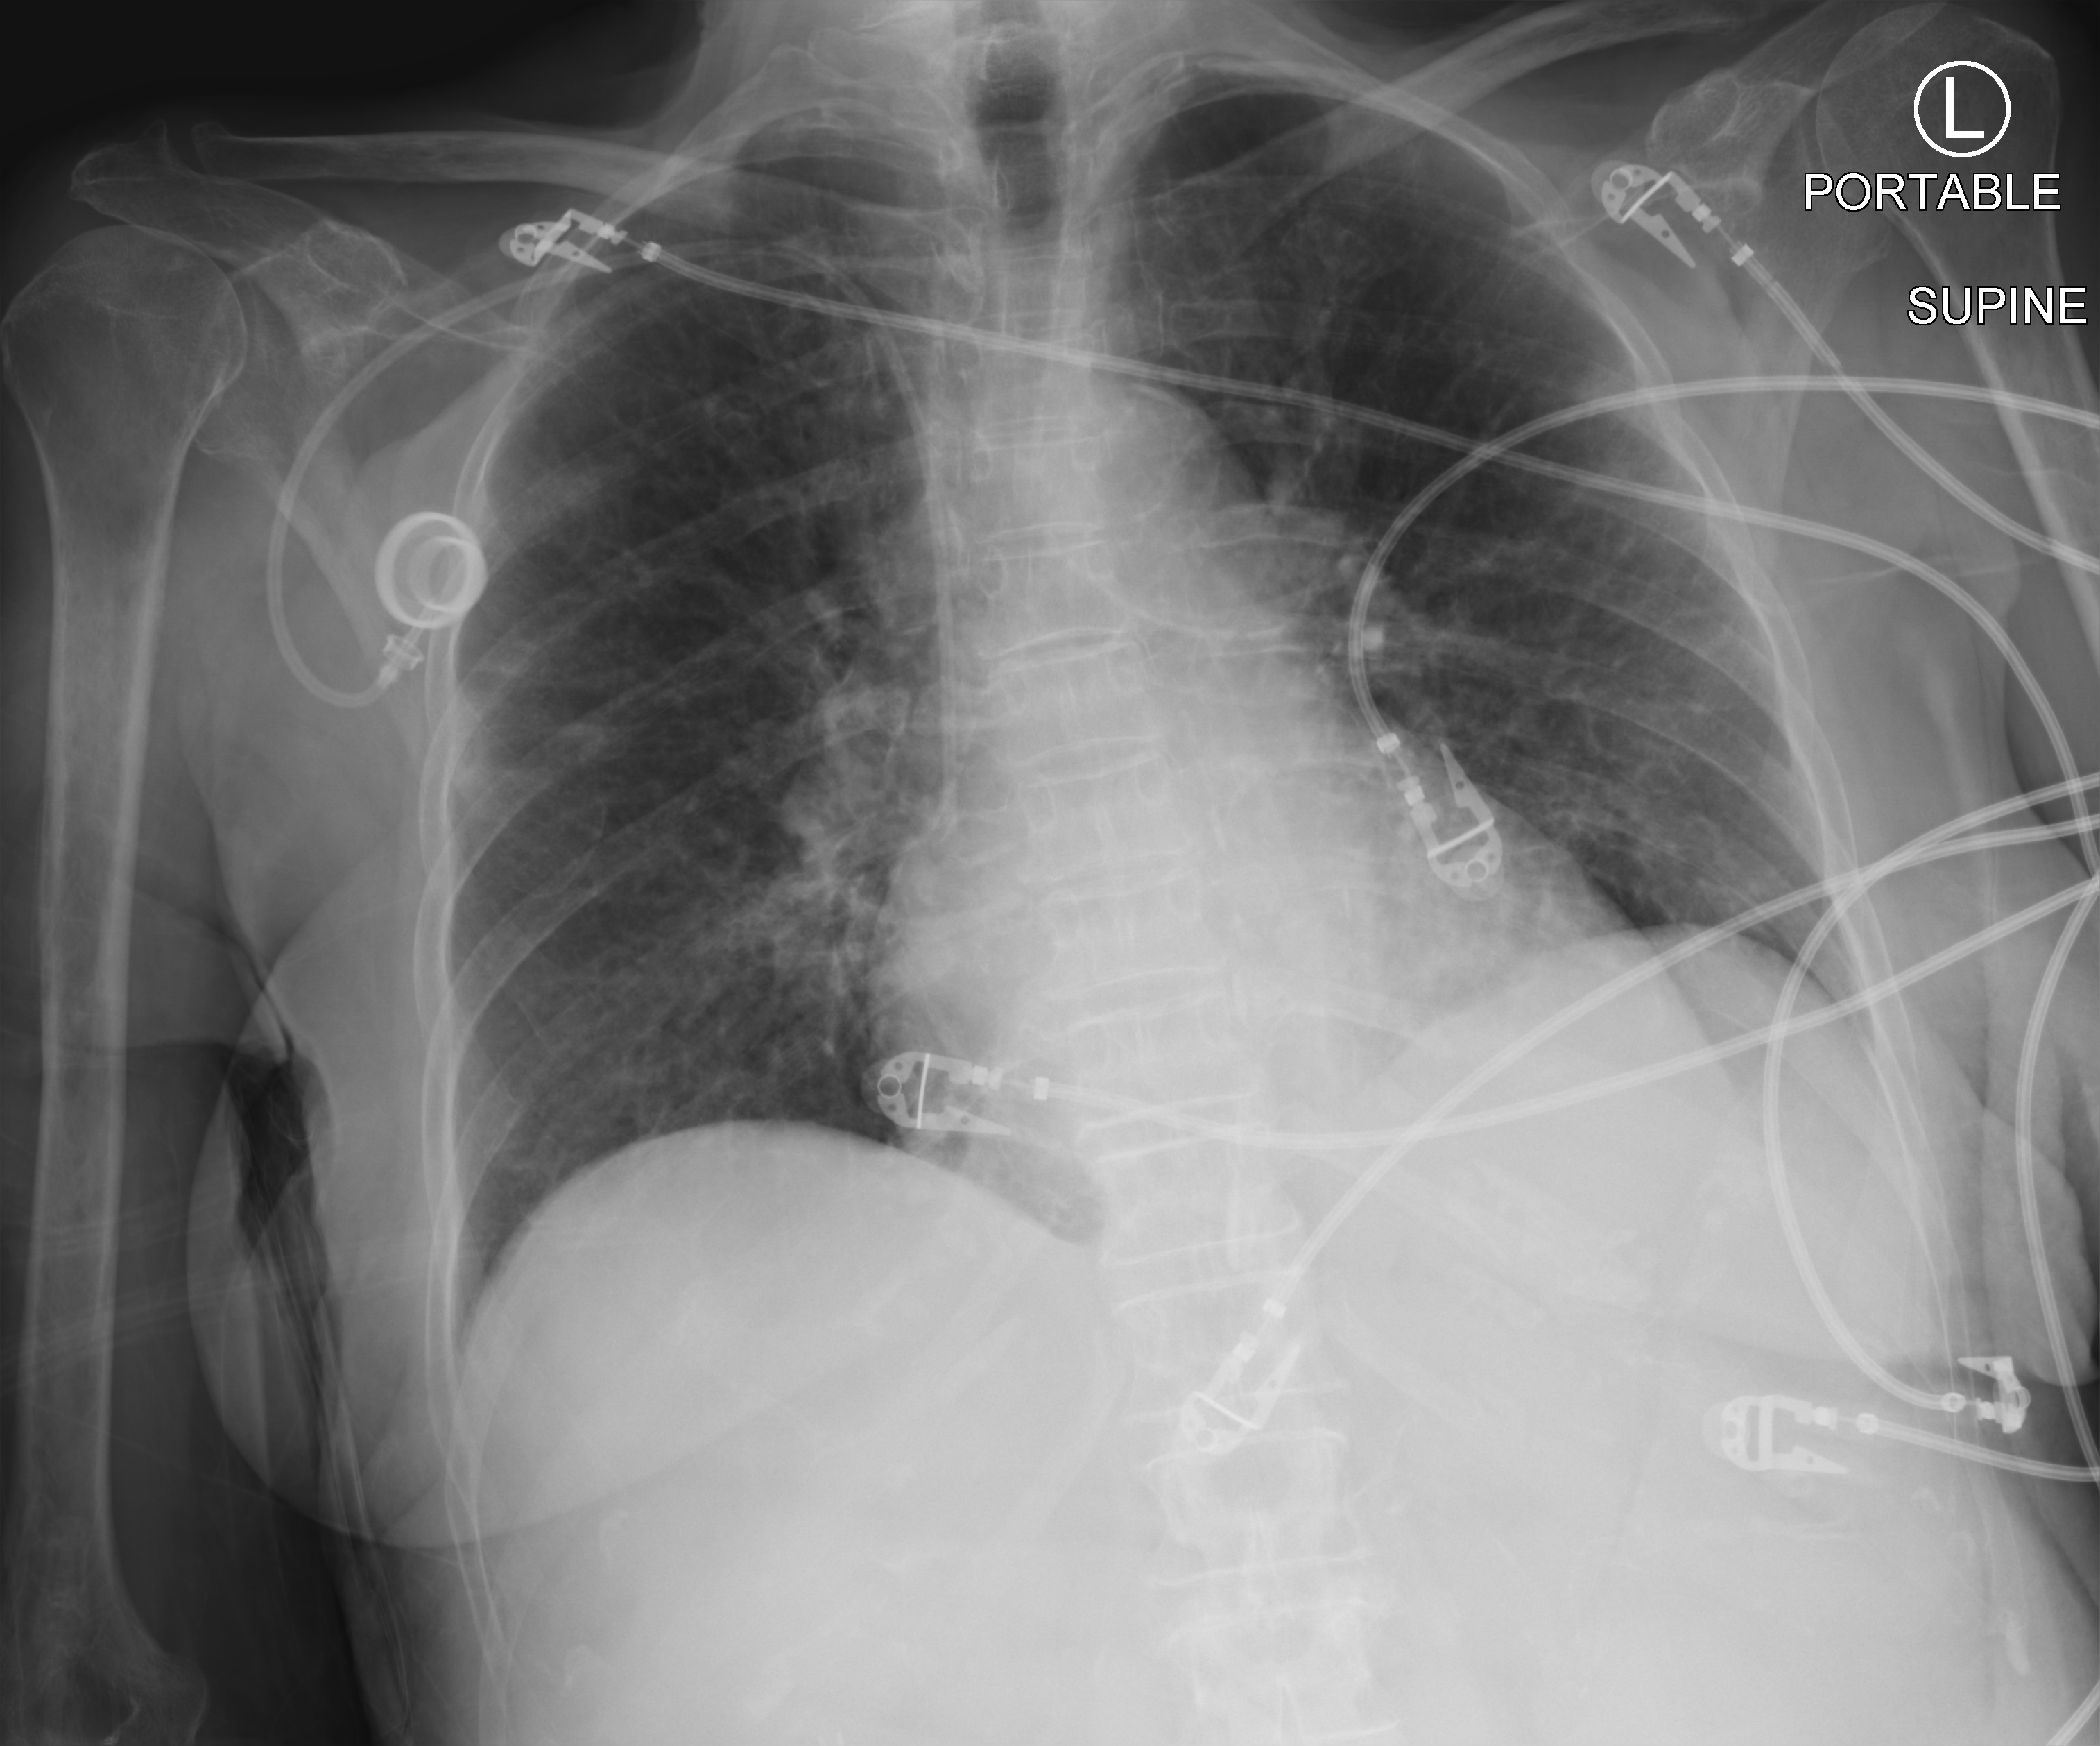
Bedside chest radiograph (computed radiography), anteroposterior (AP) projection. Female patient hospitalised with COVID-19, age 75–90 years.
Hospital-stay facts (about this admission, not read from this image; timing relative to this image not recorded):
- length of hospital stay: 7 days
- admitted to intensive care during this hospital stay: yes